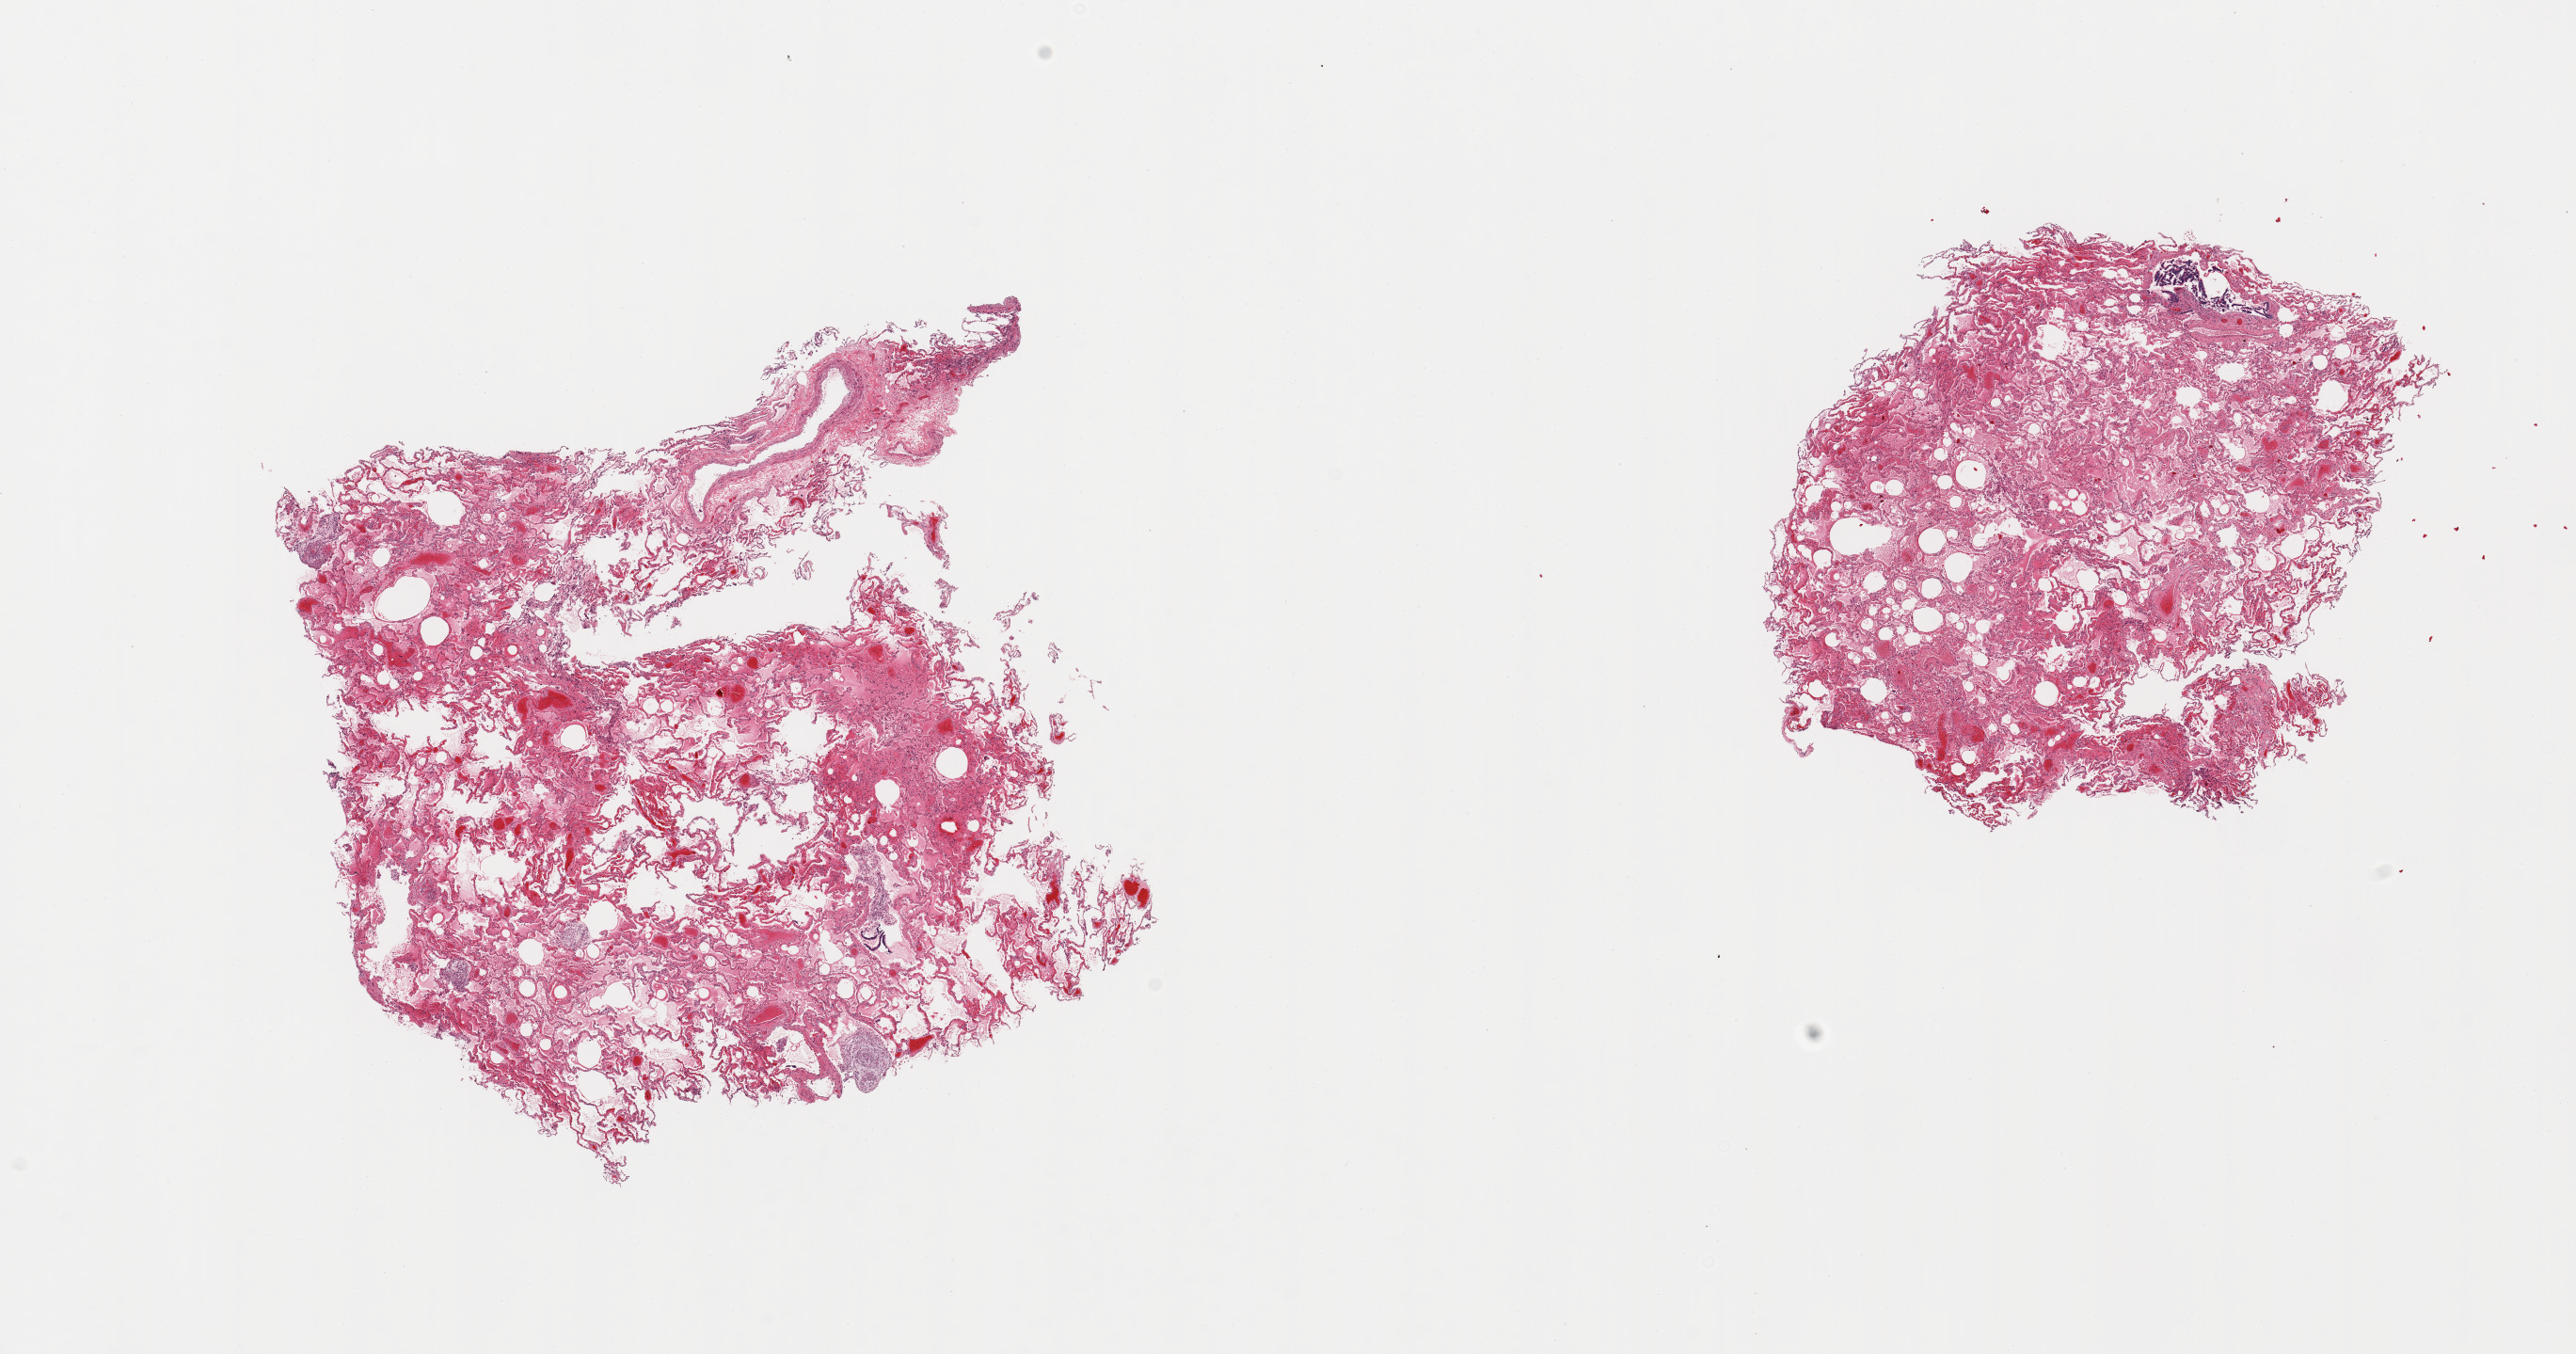
Hematoxylin and eosin (H&E) whole-slide image, whole scanned area (about 21.7 x 11.4 mm) shown as a low-resolution overview, PAXgene-fixed, paraffin-embedded tissue, section of lung (target tissue), tissue donor sample. Donor: female.
Review note (as recorded): 2 pieces; pulmonary edema & early bronchopneumonia.